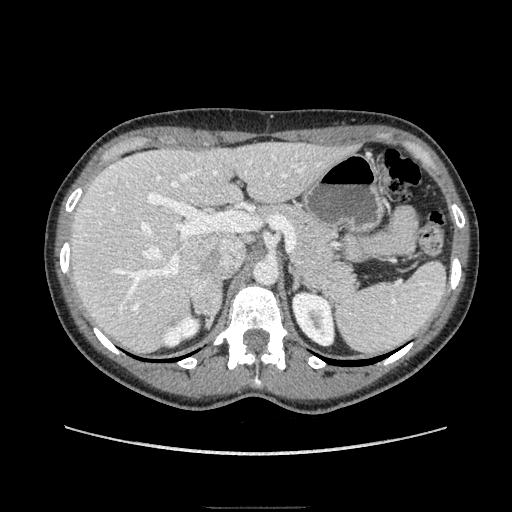
Contrast-enhanced abdominal CT, one axial slice. Slice 117 of 193 in the series (ordered by position). Soft-tissue window (W 400 / L 40 HU). 1.25 mm slice thickness. 512 × 512 image matrix, field of view 380 × 380 mm. Female patient. Case-level facts recorded for this patient, not image findings: diagnosis: adrenocortical carcinoma; tumour side: right adrenal; tumour size at pathology: 3 cm; Ki-67 index: 4 %; stage (as recorded): 1.
Outlined on this slice (semi-automatically segmented with operator editing):
- mass: bounding box <192,274,220,327> (left, top, right, bottom; pixels)